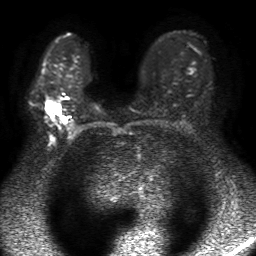
Breast MRI, one axial slice. Diffusion-weighted series; image 2 of 4 stored at this slice position (different b-values; order by instance number). 1.5 T. 256 × 256 image matrix, field of view 320 × 320 mm. Female patient.
Annotated regions visible in this slice (expert manual segmentation):
- tumour on diffusion-weighted imaging: box from (x=46, y=99) to (x=57, y=111) px